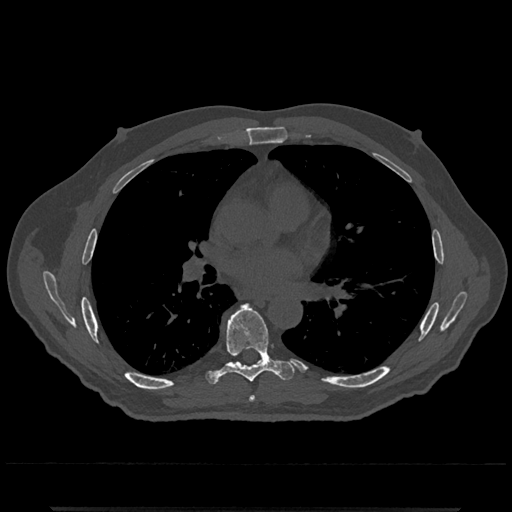
CT including the spine, one axial slice; slice 723 of 797 in the series (ordered by position); reconstruction kernel Br40s/3; 120 kVp; bone window (W 1800 / L 400 HU); 0.5 mm slice thickness; 512 × 512 image matrix. Patient: male, 67 years. From the clinical record (not read from this slice): primary cancer: prostate.
Outlined on this slice (semi-automatic segmentation, software-assisted and operator-edited):
- T6 vertebra: bounding box [x1, y1, x2, y2] px = [249, 396, 256, 402]
- T7 vertebra: [208, 304, 294, 384]